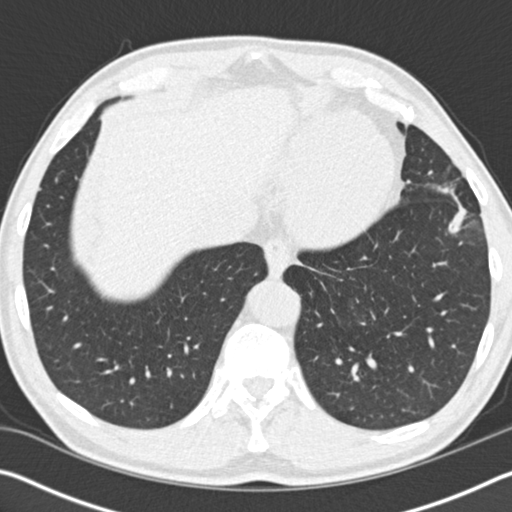
Low-dose screening chest CT, one axial slice. Reconstruction kernel B30f. Lung window (W 1500 / L -600 HU). 2 mm slice thickness. 512 × 512 image matrix.
Outlined on this slice (manually delineated by an expert):
- lesion 1 (tumor, upper lobe of left lung): box from (x=439, y=187) to (x=467, y=234) px